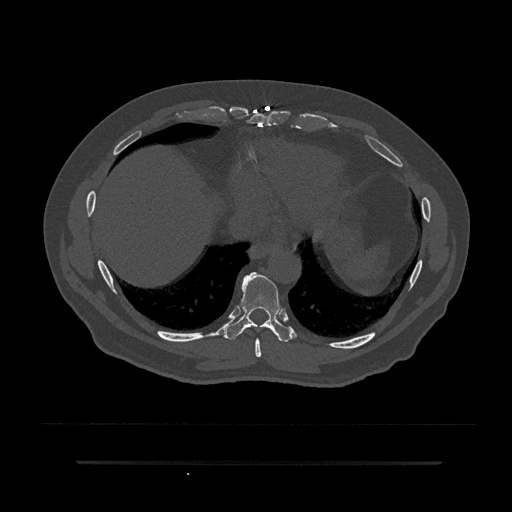
CT including the spine, one axial slice. Reconstruction kernel Br40s/3. 120 kVp. Bone window (W 1800 / L 400 HU). 0.5 mm slice thickness. 512 × 512 image matrix. Patient: male, 59 years. From the clinical record (not read from this slice): primary cancer: bile ducts.
Annotated regions visible in this slice (semi-automatic segmentation, software-assisted and operator-edited):
- T8 vertebra: box from (x=255, y=338) to (x=262, y=357) px
- T9 vertebra: (x=226, y=272)–(x=292, y=342)